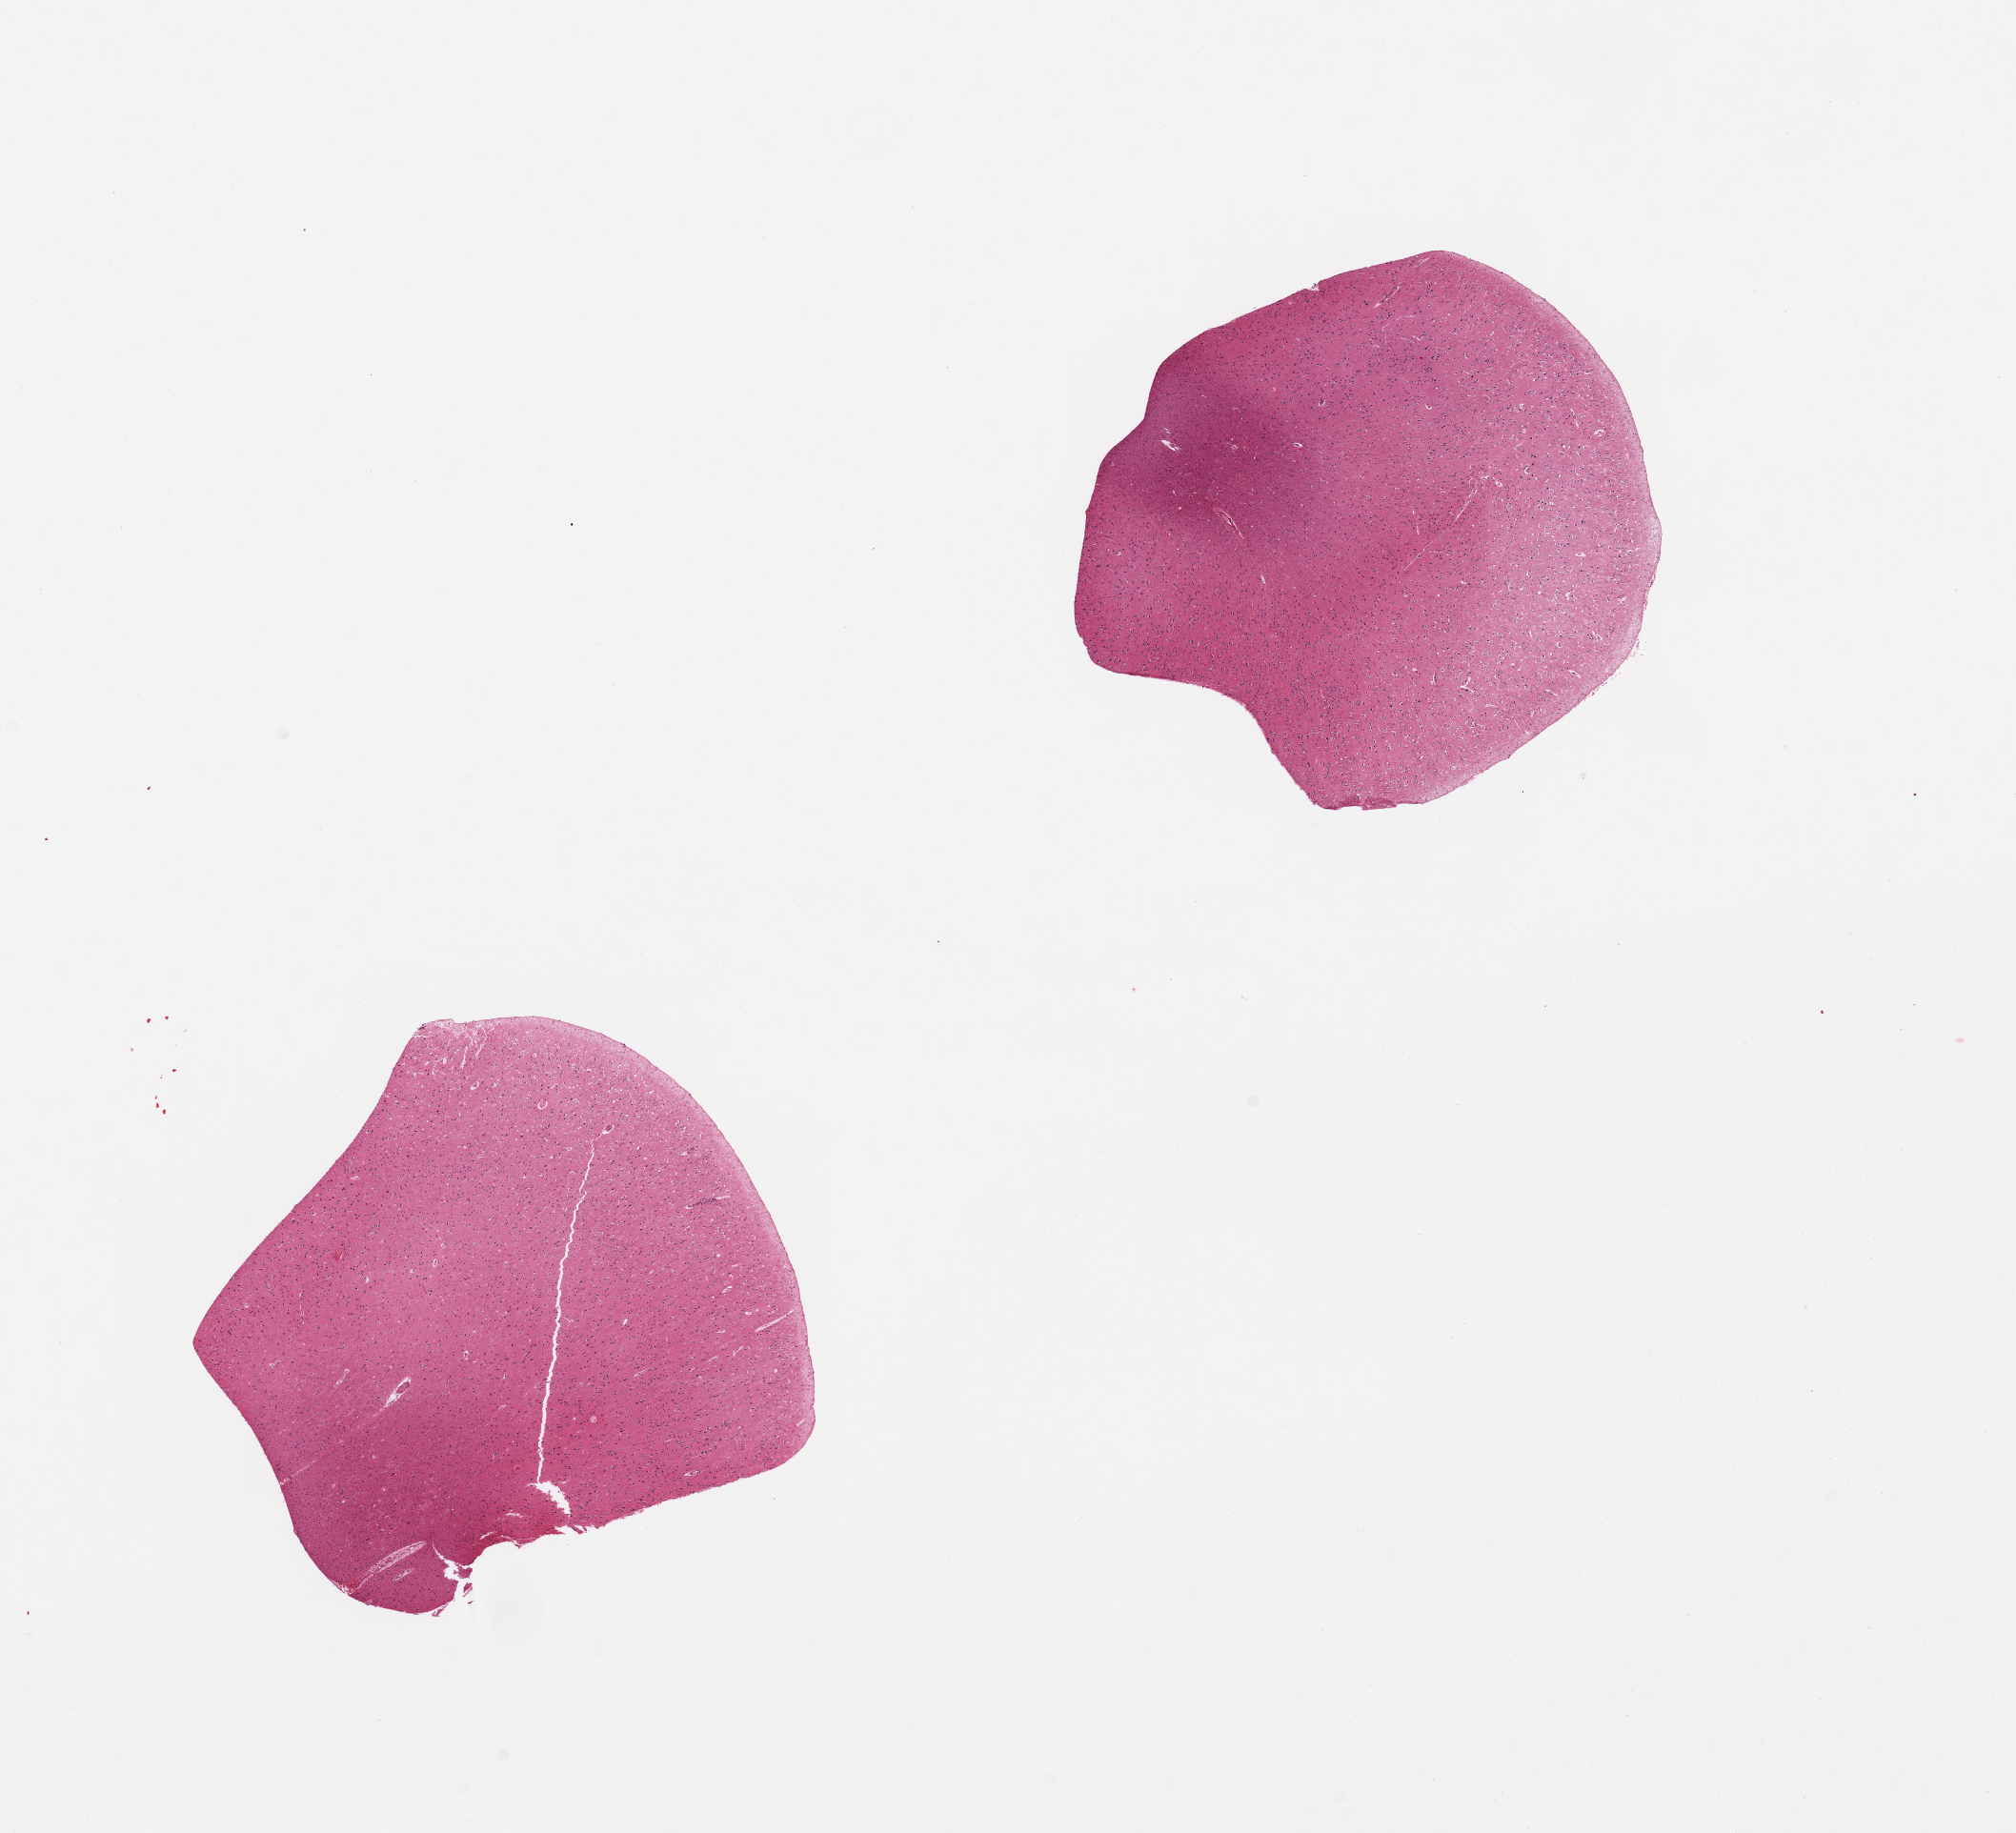
Whole-slide image, H&E stain, low-resolution overview of the scanned area, about 16.7 x 15.2 mm (slide scanned at 20x); PAXgene-fixed, paraffin-embedded tissue; section of cerebral cortex (target tissue); donor tissue sample. Male donor.
Pathologist's review note for this sample: 2 pieces.